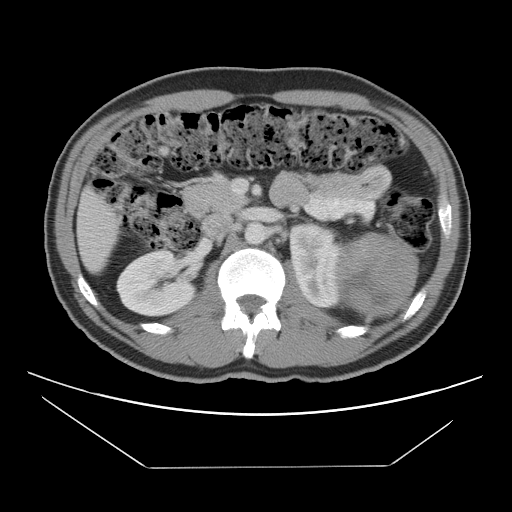
Contrast-enhanced abdominal CT, one axial slice. Reconstruction kernel STANDARD. 120 kVp. Soft-tissue window (W 400 / L 40 HU). 5 mm slice thickness. 512 × 512 image matrix, field of view 396 × 396 mm. Patient: male, 44 years. From the clinical record (not read from this slice): diagnosis: adrenocortical carcinoma; tumour side: left adrenal; tumour size at pathology: 15.5 cm; Ki-67 index: 6 %; stage (as recorded): 2.
Annotated regions visible in this slice (semi-automatic segmentation, software-assisted and operator-edited):
- mass: bounding box [x1, y1, x2, y2] px = [337, 233, 416, 315]